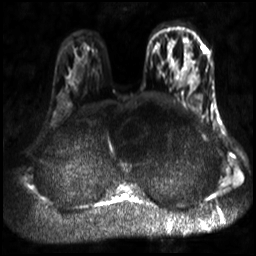
Breast MRI, one axial slice. Position 22 of 30 along the scan axis. Diffusion-weighted series; image 2 of 4 stored at this slice position (different b-values; order by instance number). 3 T. 256 × 256 image matrix, field of view 320 × 320 mm. Female patient.
Annotated regions visible in this slice (manually delineated by an expert):
- tumour on diffusion-weighted imaging: bounding box [x1, y1, x2, y2] px = [189, 72, 198, 84]